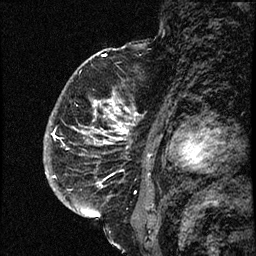
Breast MRI (dynamic contrast-enhanced), one sagittal slice; position 49 of 66 along the scan axis; dynamic contrast-enhanced study with each time point stored as its own series, time point 2 of 3 at this slice position (early post-contrast, ordered by acquisition time); 1.5 T; TE 4.2 ms, TR 17.6 ms; 2 mm slice thickness; 256 × 256 image matrix. Female patient. From the clinical record (not read from this slice): setting: breast cancer imaged before/during neoadjuvant chemotherapy; receptor status: HER2-positive.
Annotated regions visible in this slice (semi-automatic segmentation, software-assisted and operator-edited):
- analysis volume of interest (the breast-tissue region the enhancement analysis was run in; not a lesion): box from (x=52, y=69) to (x=139, y=209) px
- tumour enhancement mask (voxels above the 100 % enhancement threshold inside the analysis volume of interest): (x=52, y=98)–(x=136, y=187)